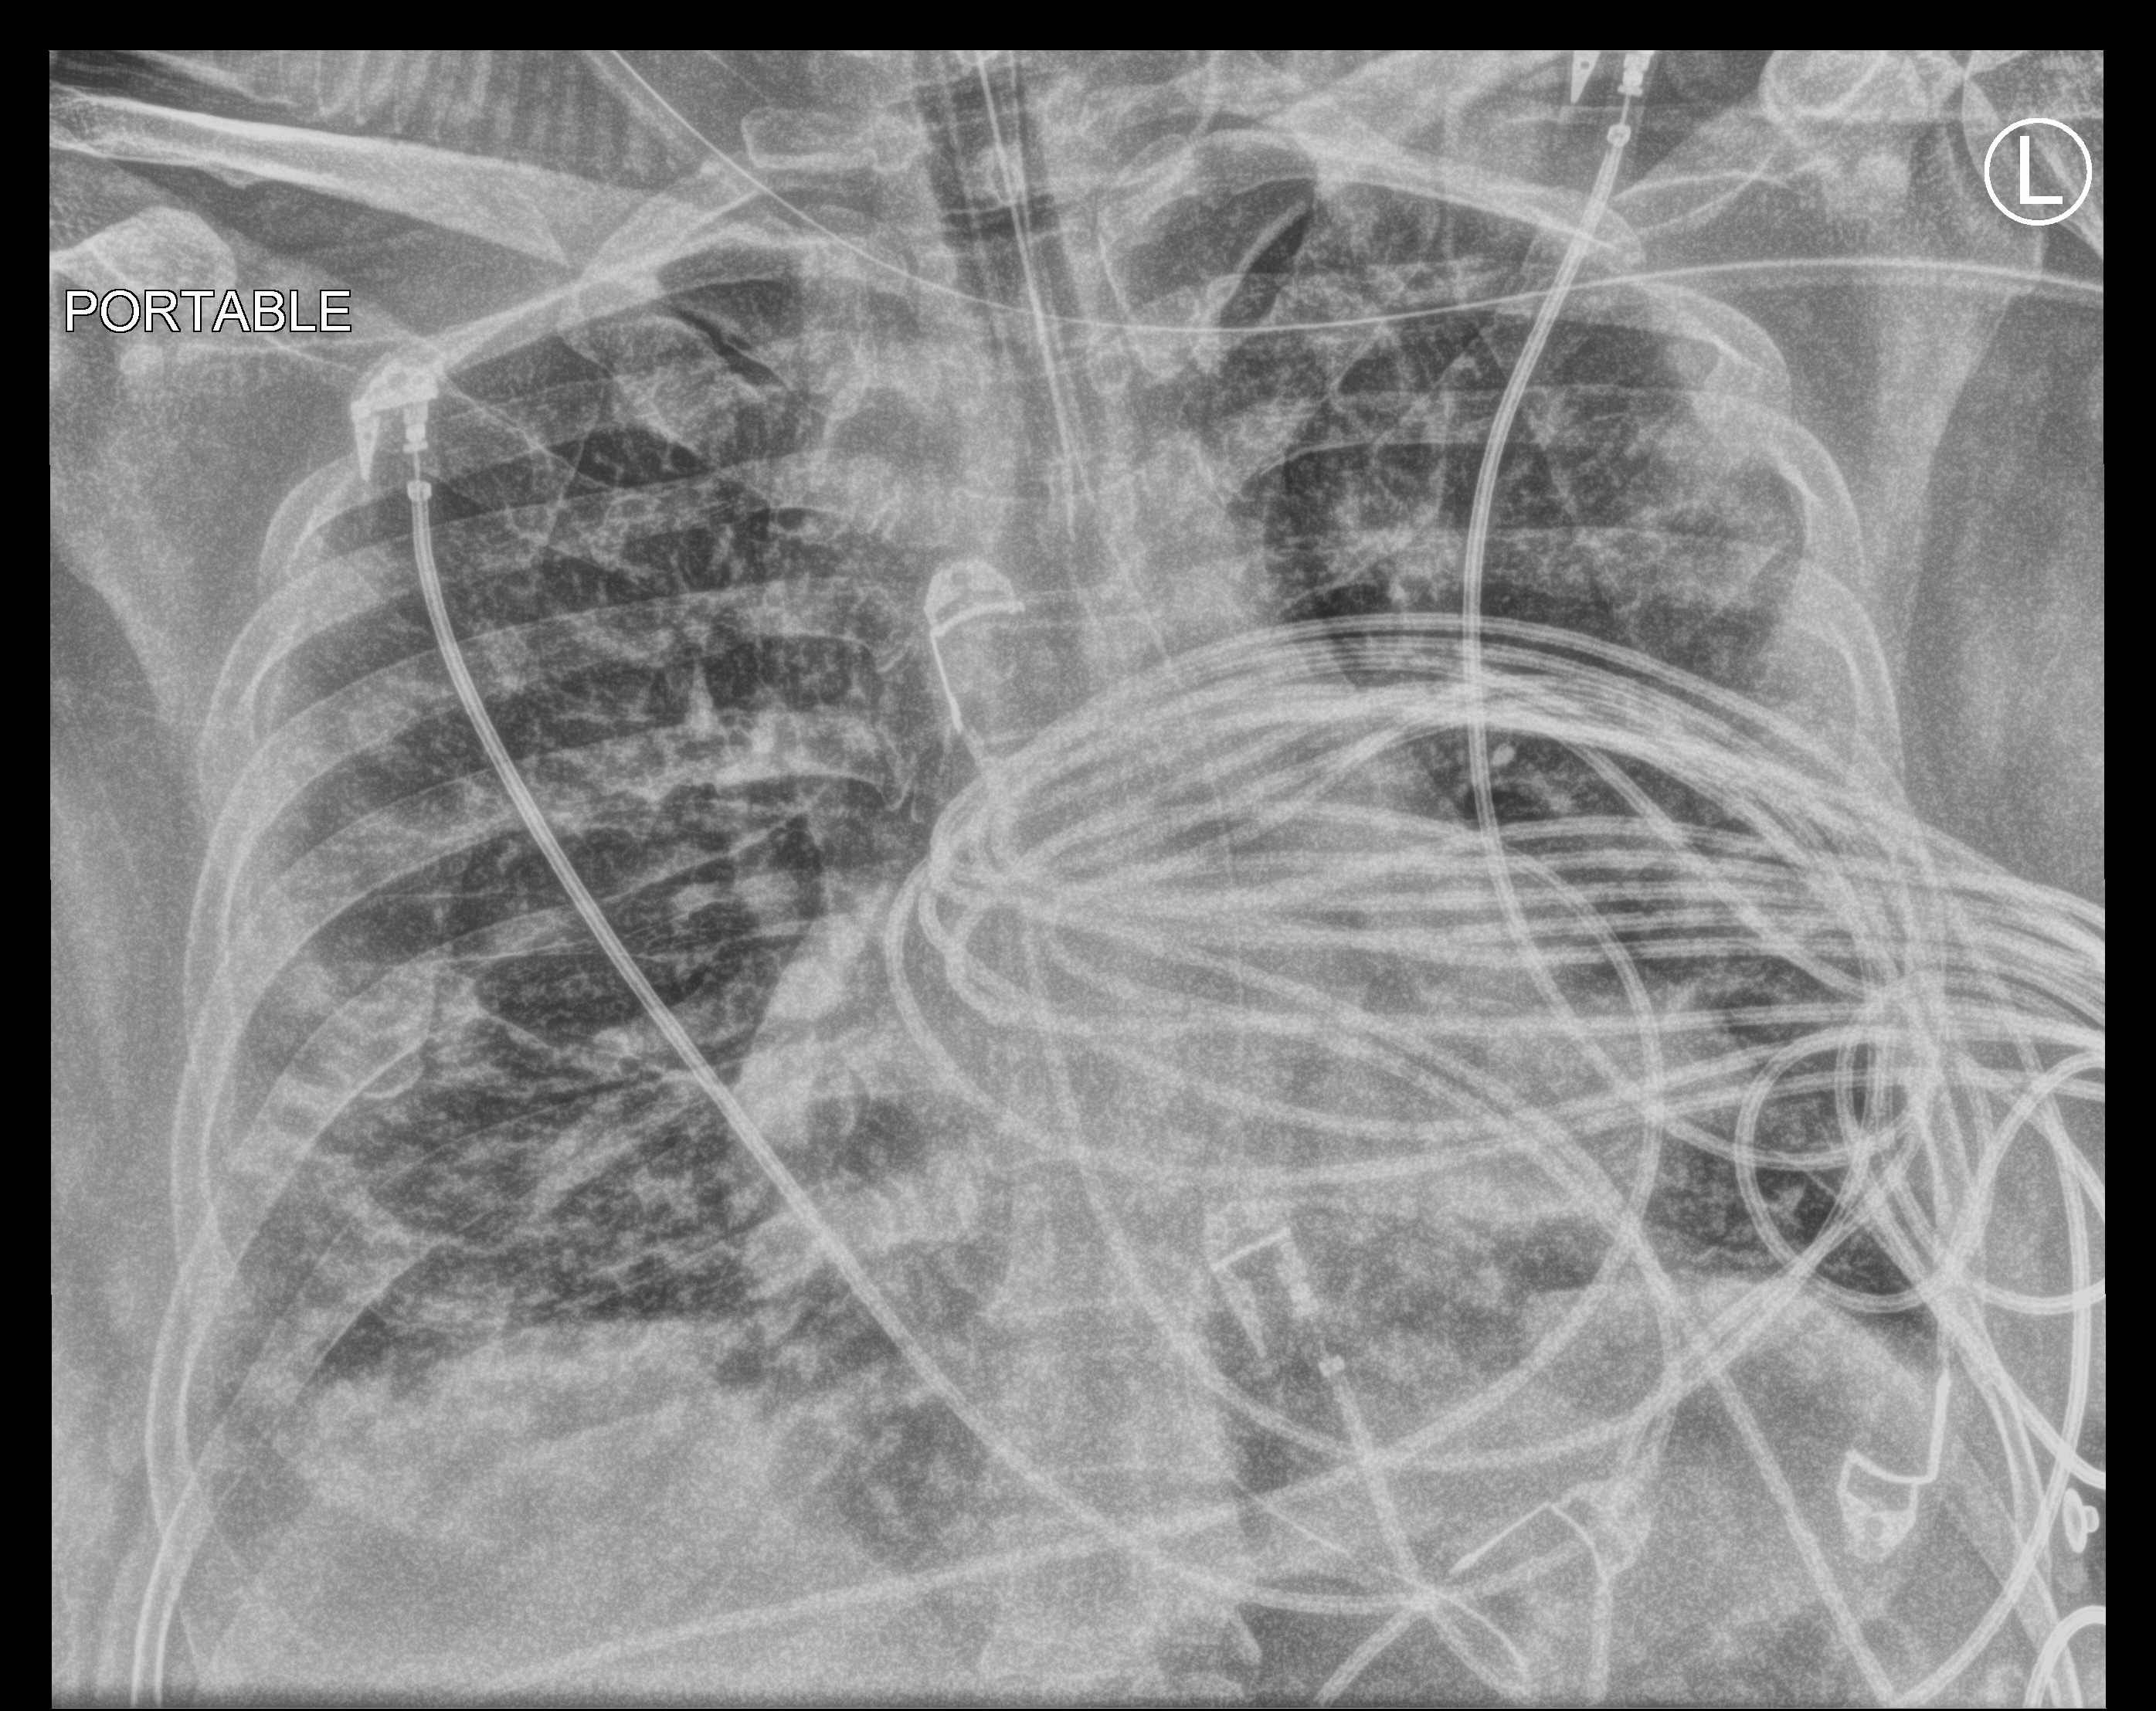
Portable chest radiograph, anteroposterior (AP) projection. Patient hospitalised with COVID-19; male, aged 18–59 years.
From the hospital-stay record, not from the radiograph (when in the stay this image was taken is not recorded): mechanically ventilated during this hospital stay: yes.